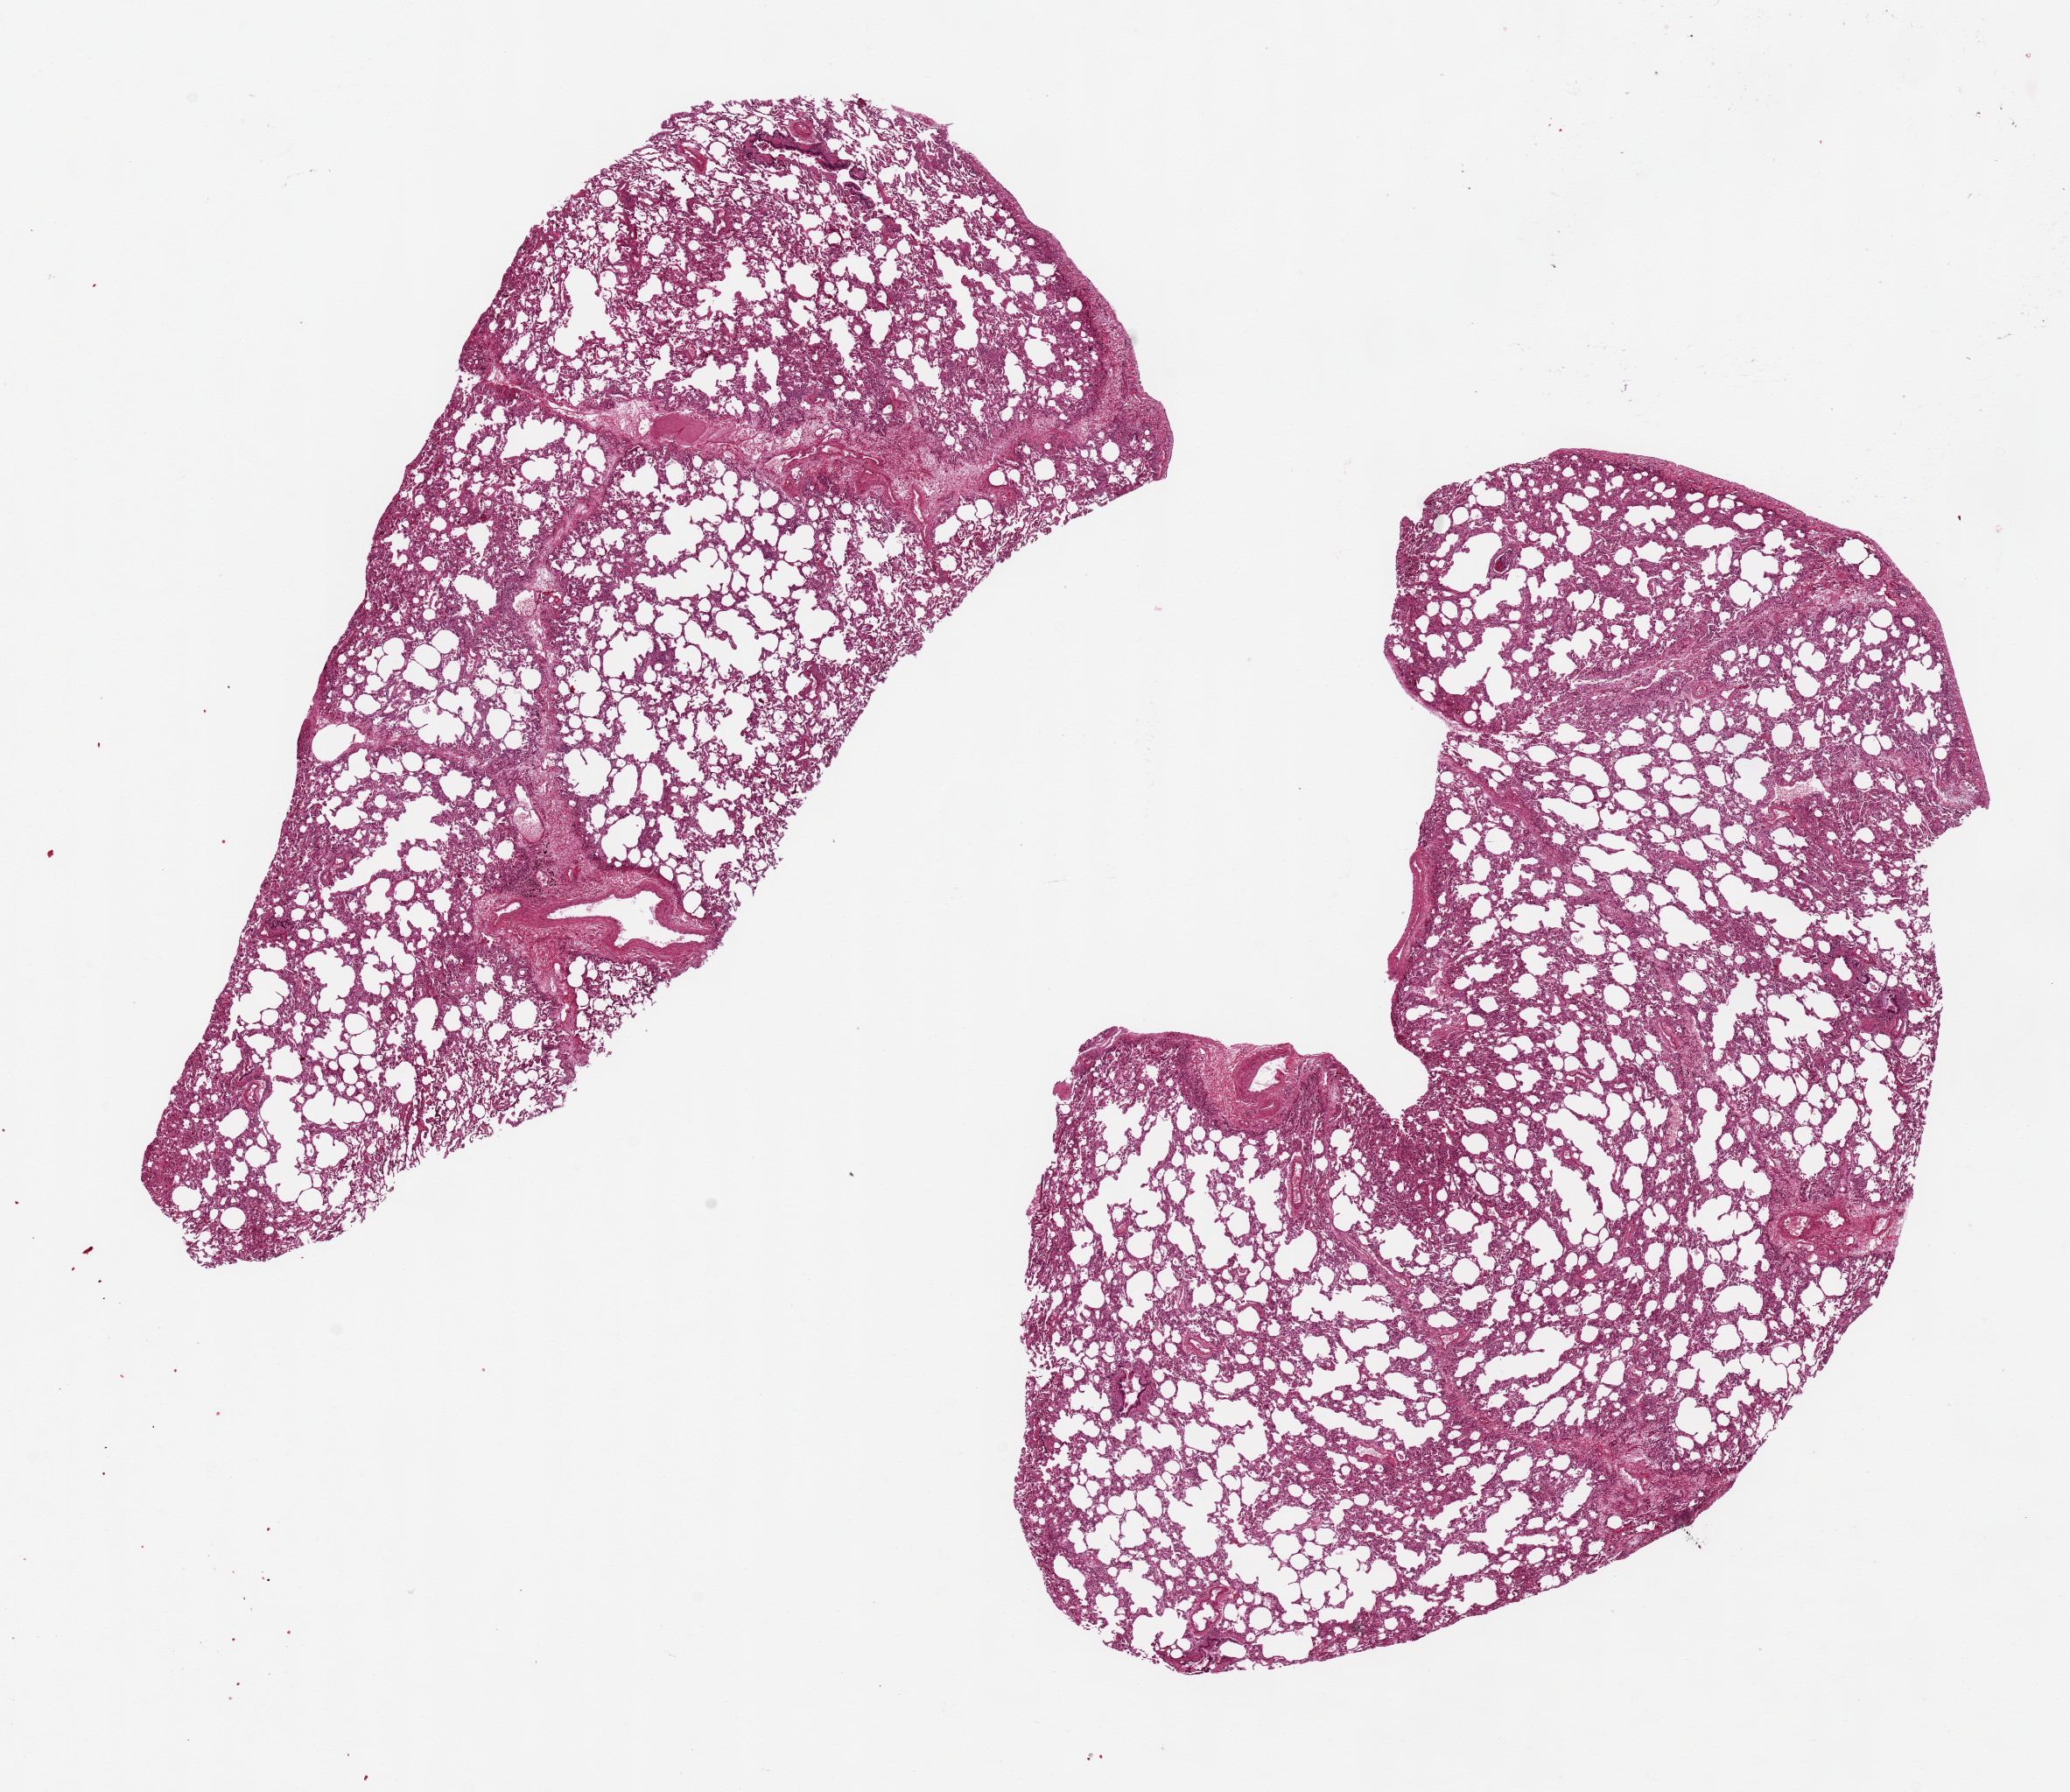
Whole-slide image, haematoxylin and eosin stain, brightfield, low-resolution overview of the scanned area, about 18.7 x 16.2 mm (slide scanned at 20x). PAXgene-fixed paraffin-embedded (PFPE) section. Sampled site (target tissue): lung. Tissue donor sample. Female donor.
Review note (as recorded): 2 pieces, up to 12x6 mm.